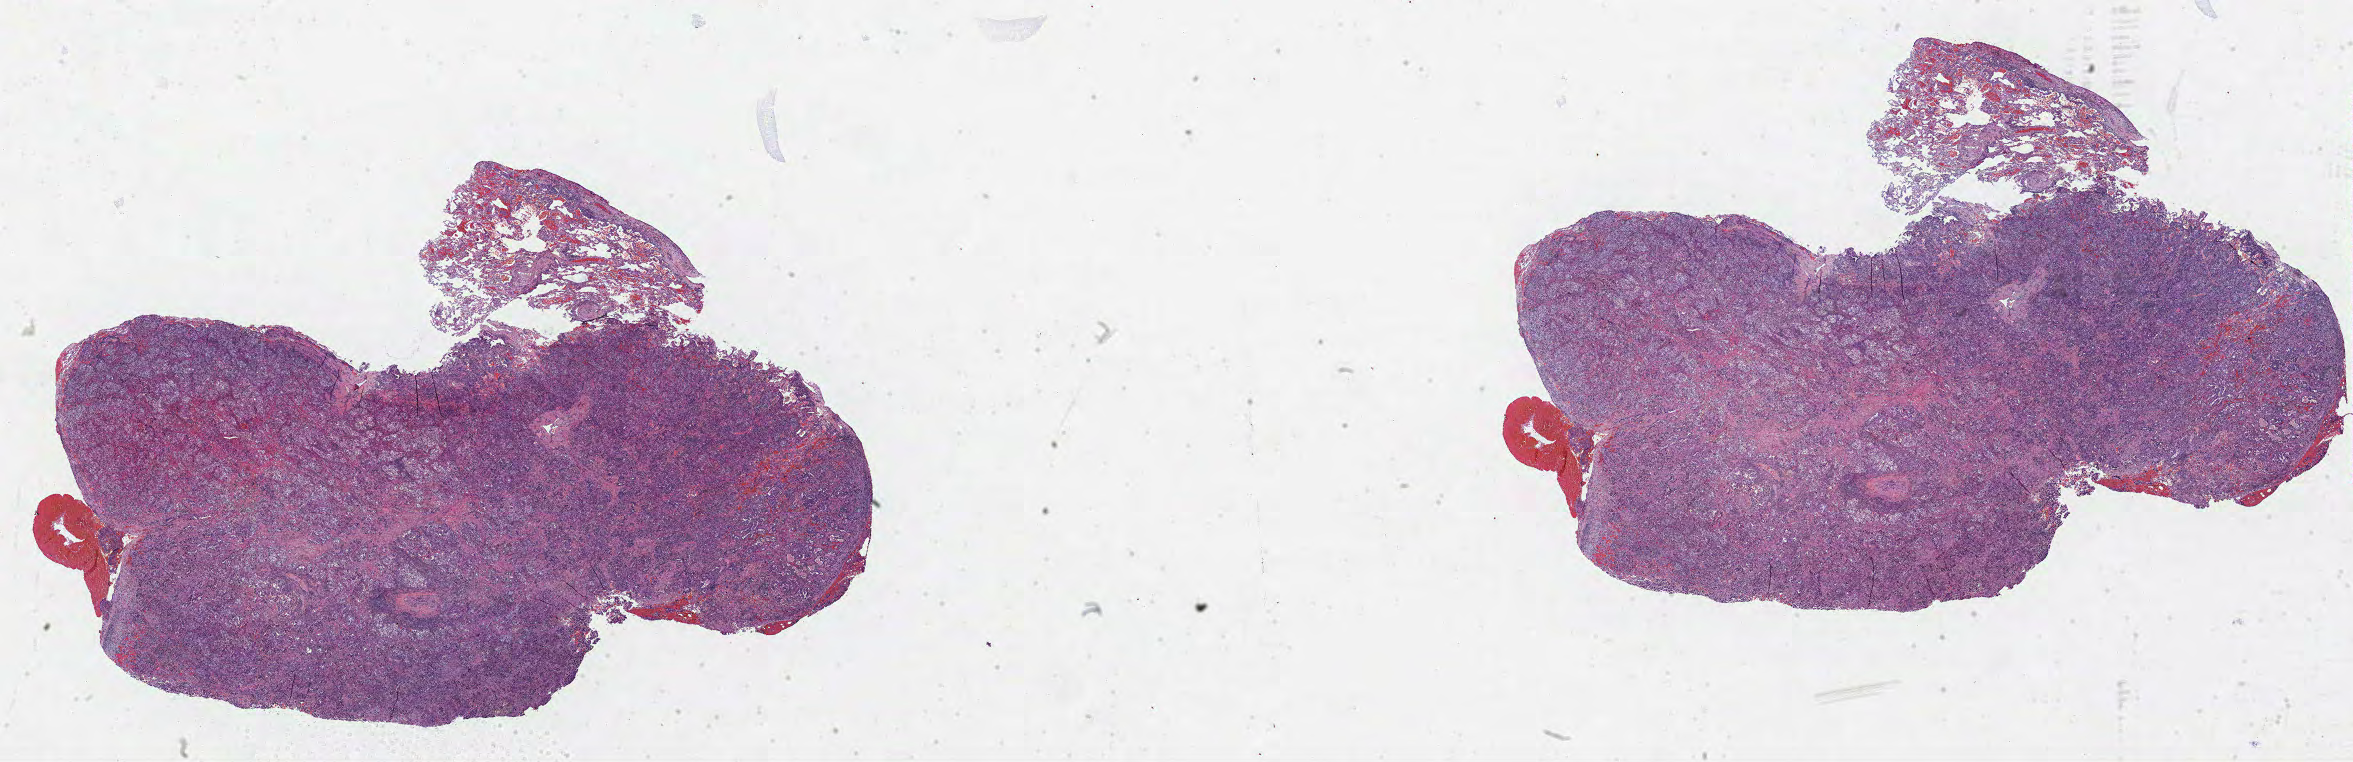
Whole-slide histology image, H&E-stained — shown as a low-resolution overview of the whole scanned area (about 38.0 x 12.3 mm, acquisition: 40x scan). Formalin-fixed paraffin-embedded (FFPE) diagnostic section. Sample: primary tumour, lung. Female patient; age at initial diagnosis 60 years.
AJCC pathologic stage: IA. Histologic diagnosis: Adenocarcinoma, NOS.